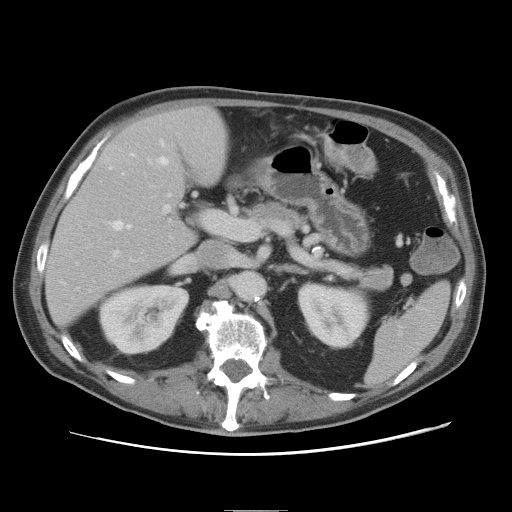
Contrast-enhanced abdominal CT, one axial slice. Position 40 of 89 along the scan axis. 120 kVp. Intravenous contrast given. Soft-tissue window (W 400 / L 40 HU). 5 mm slice thickness. 512 × 512 image matrix, field of view 375 × 375 mm. Male patient, age 69 years. Case-level facts recorded for this patient, not image findings: diagnosis: colorectal cancer liver metastases, imaged before liver resection; multiple liver metastases: no; largest metastasis: 8.5 cm.
Structures marked on this image (outlined manually by an expert reader):
- hepatic veins: bounding box (x1, y1, x2, y2) in pixels: (111, 140, 171, 230)
- liver: (46, 107, 229, 324)
- planned liver remnant (the part of the liver to remain after resection): (46, 107, 229, 324)
- portal vein (with intrahepatic branches): (114, 161, 224, 255)